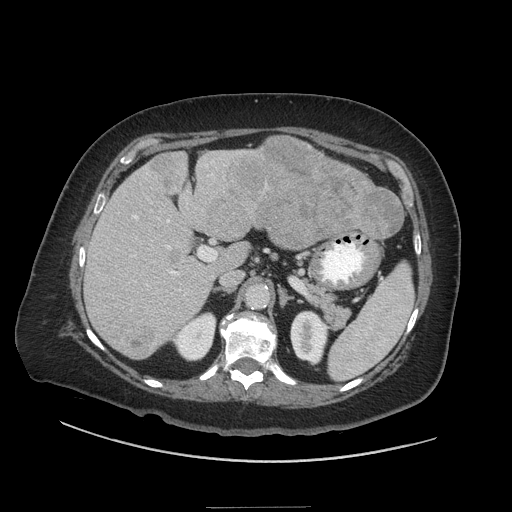
Contrast-enhanced abdominal CT (liver protocol), one axial slice. Slice 23 of 81 in the series (ordered by position). Reconstruction kernel STANDARD. 140 kVp. Soft-tissue window (W 400 / L 40 HU). 2.5 mm slice thickness. 512 × 512 image matrix, field of view 440 × 440 mm. Case-level facts recorded for this patient, not image findings: diagnosis: hepatocellular carcinoma (patient treated with transarterial chemoembolisation; whether this scan precedes or follows treatment is not stated here); TNM stage (as recorded): Stage-II; Child-Pugh class: A; tumour differentiation: moderately differentiated.
Structures marked on this image (semi-automatically segmented with operator editing):
- liver parenchyma outside the tumour (the mass and vessels are separate outlines, so this box may not span the whole liver): box from (x=84, y=136) to (x=400, y=358) px
- mass: (x=129, y=139)–(x=402, y=357)
- liver vessels: (x=130, y=165)–(x=213, y=311)